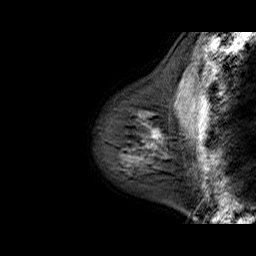
Breast MRI (dynamic contrast-enhanced), one sagittal slice. Slice 17 of 60 in the series (ordered by position). Dynamic contrast-enhanced series, time point 2 of 6 at this slice position (early post-contrast). 1.5 T. TE 6.4 ms, TR 32.9 ms. 256 × 256 image matrix. Female patient. Case-level facts recorded for this patient, not image findings: setting: breast cancer imaged before/during neoadjuvant chemotherapy; receptor status: HR-positive, HER2-negative.
Annotated regions visible in this slice (semi-automatic segmentation, software-assisted and operator-edited):
- analysis volume of interest (the breast-tissue region the enhancement analysis was run in; not a lesion): bounding box (x1, y1, x2, y2) in pixels: (117, 108, 168, 175)
- tumour enhancement mask (voxels above the 100 % enhancement threshold inside the analysis volume of interest): (152, 129, 159, 137)